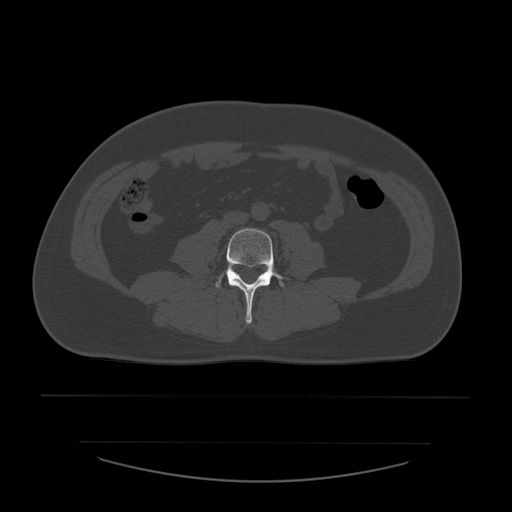
CT including the spine, one axial slice. Position 147 of 532 along the scan axis. Bone window (W 1800 / L 400 HU). 1.25 mm slice thickness. 512 × 512 image matrix, field of view 441 × 441 mm. Patient age 44 years. From the clinical record (not read from this slice): primary cancer: soft tissue sarcoma.
Outlined on this slice (semi-automatic segmentation, software-assisted and operator-edited):
- L4 vertebra: bounding box [x1, y1, x2, y2] px = [216, 229, 289, 324]